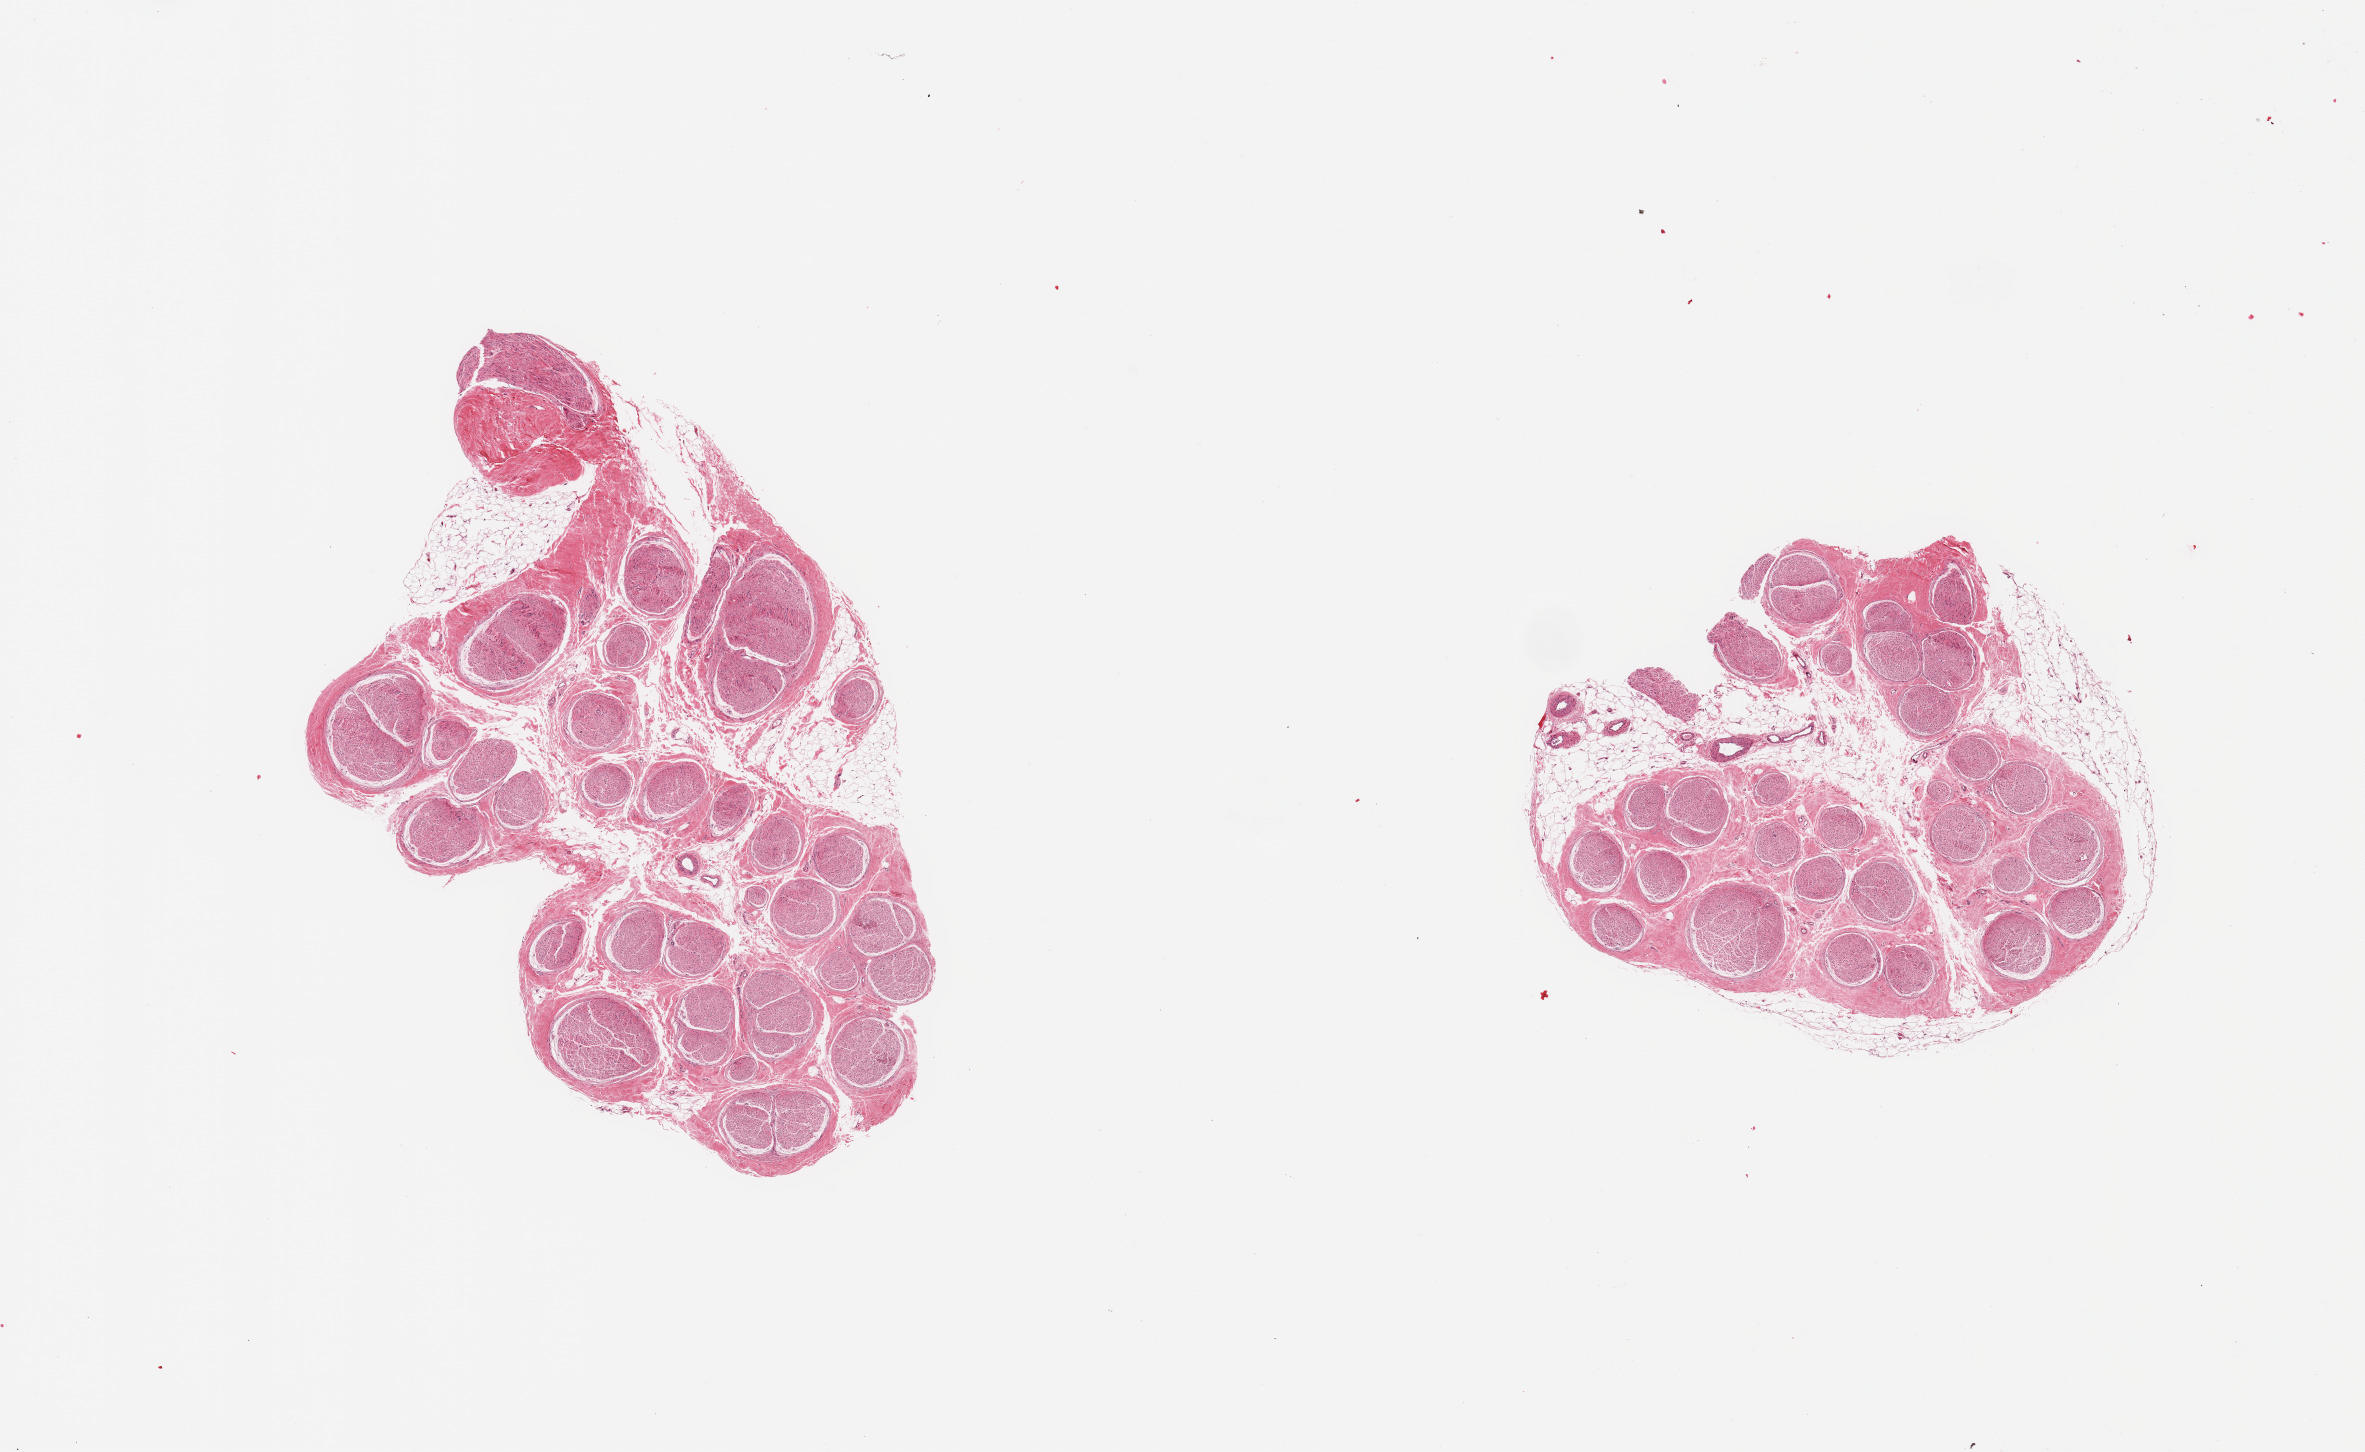
Whole-slide image, hematoxylin and eosin (H&E) stain — whole scanned area (about 18.7 x 11.5 mm, slide scanned at 20x) shown as a low-resolution overview, PAXgene-fixed paraffin-embedded (PFPE) section, section of tibial nerve (target tissue), tissue donor sample. Donor: male.
Reviewer comment on this tissue sample: 2 pieces, trace nubbin of adherent fat, <0.5mm.